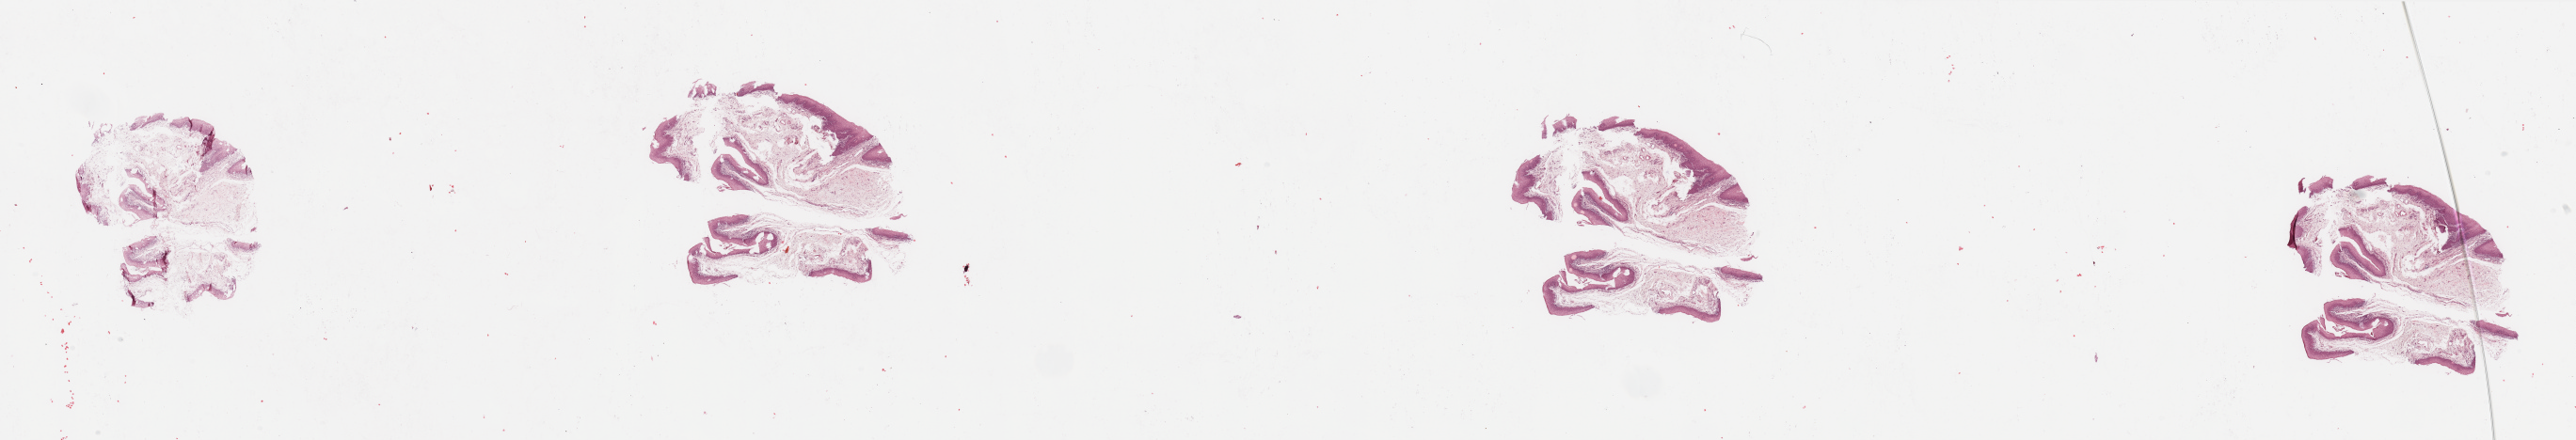
Digitized Hematoxylin and eosin (H&E) stained tissue section (whole slide) — low-resolution overview of the scanned area, about 43.3 x 7.4 mm (from a 20x scan); normal (non-tumour) tissue sample, sampled site: larynx. Male, 72 y/o.
This section: normal (non-tumour) tissue from the same patient. Patient diagnosis: Squamous cell carcinoma, NOS (larynx, NOS).